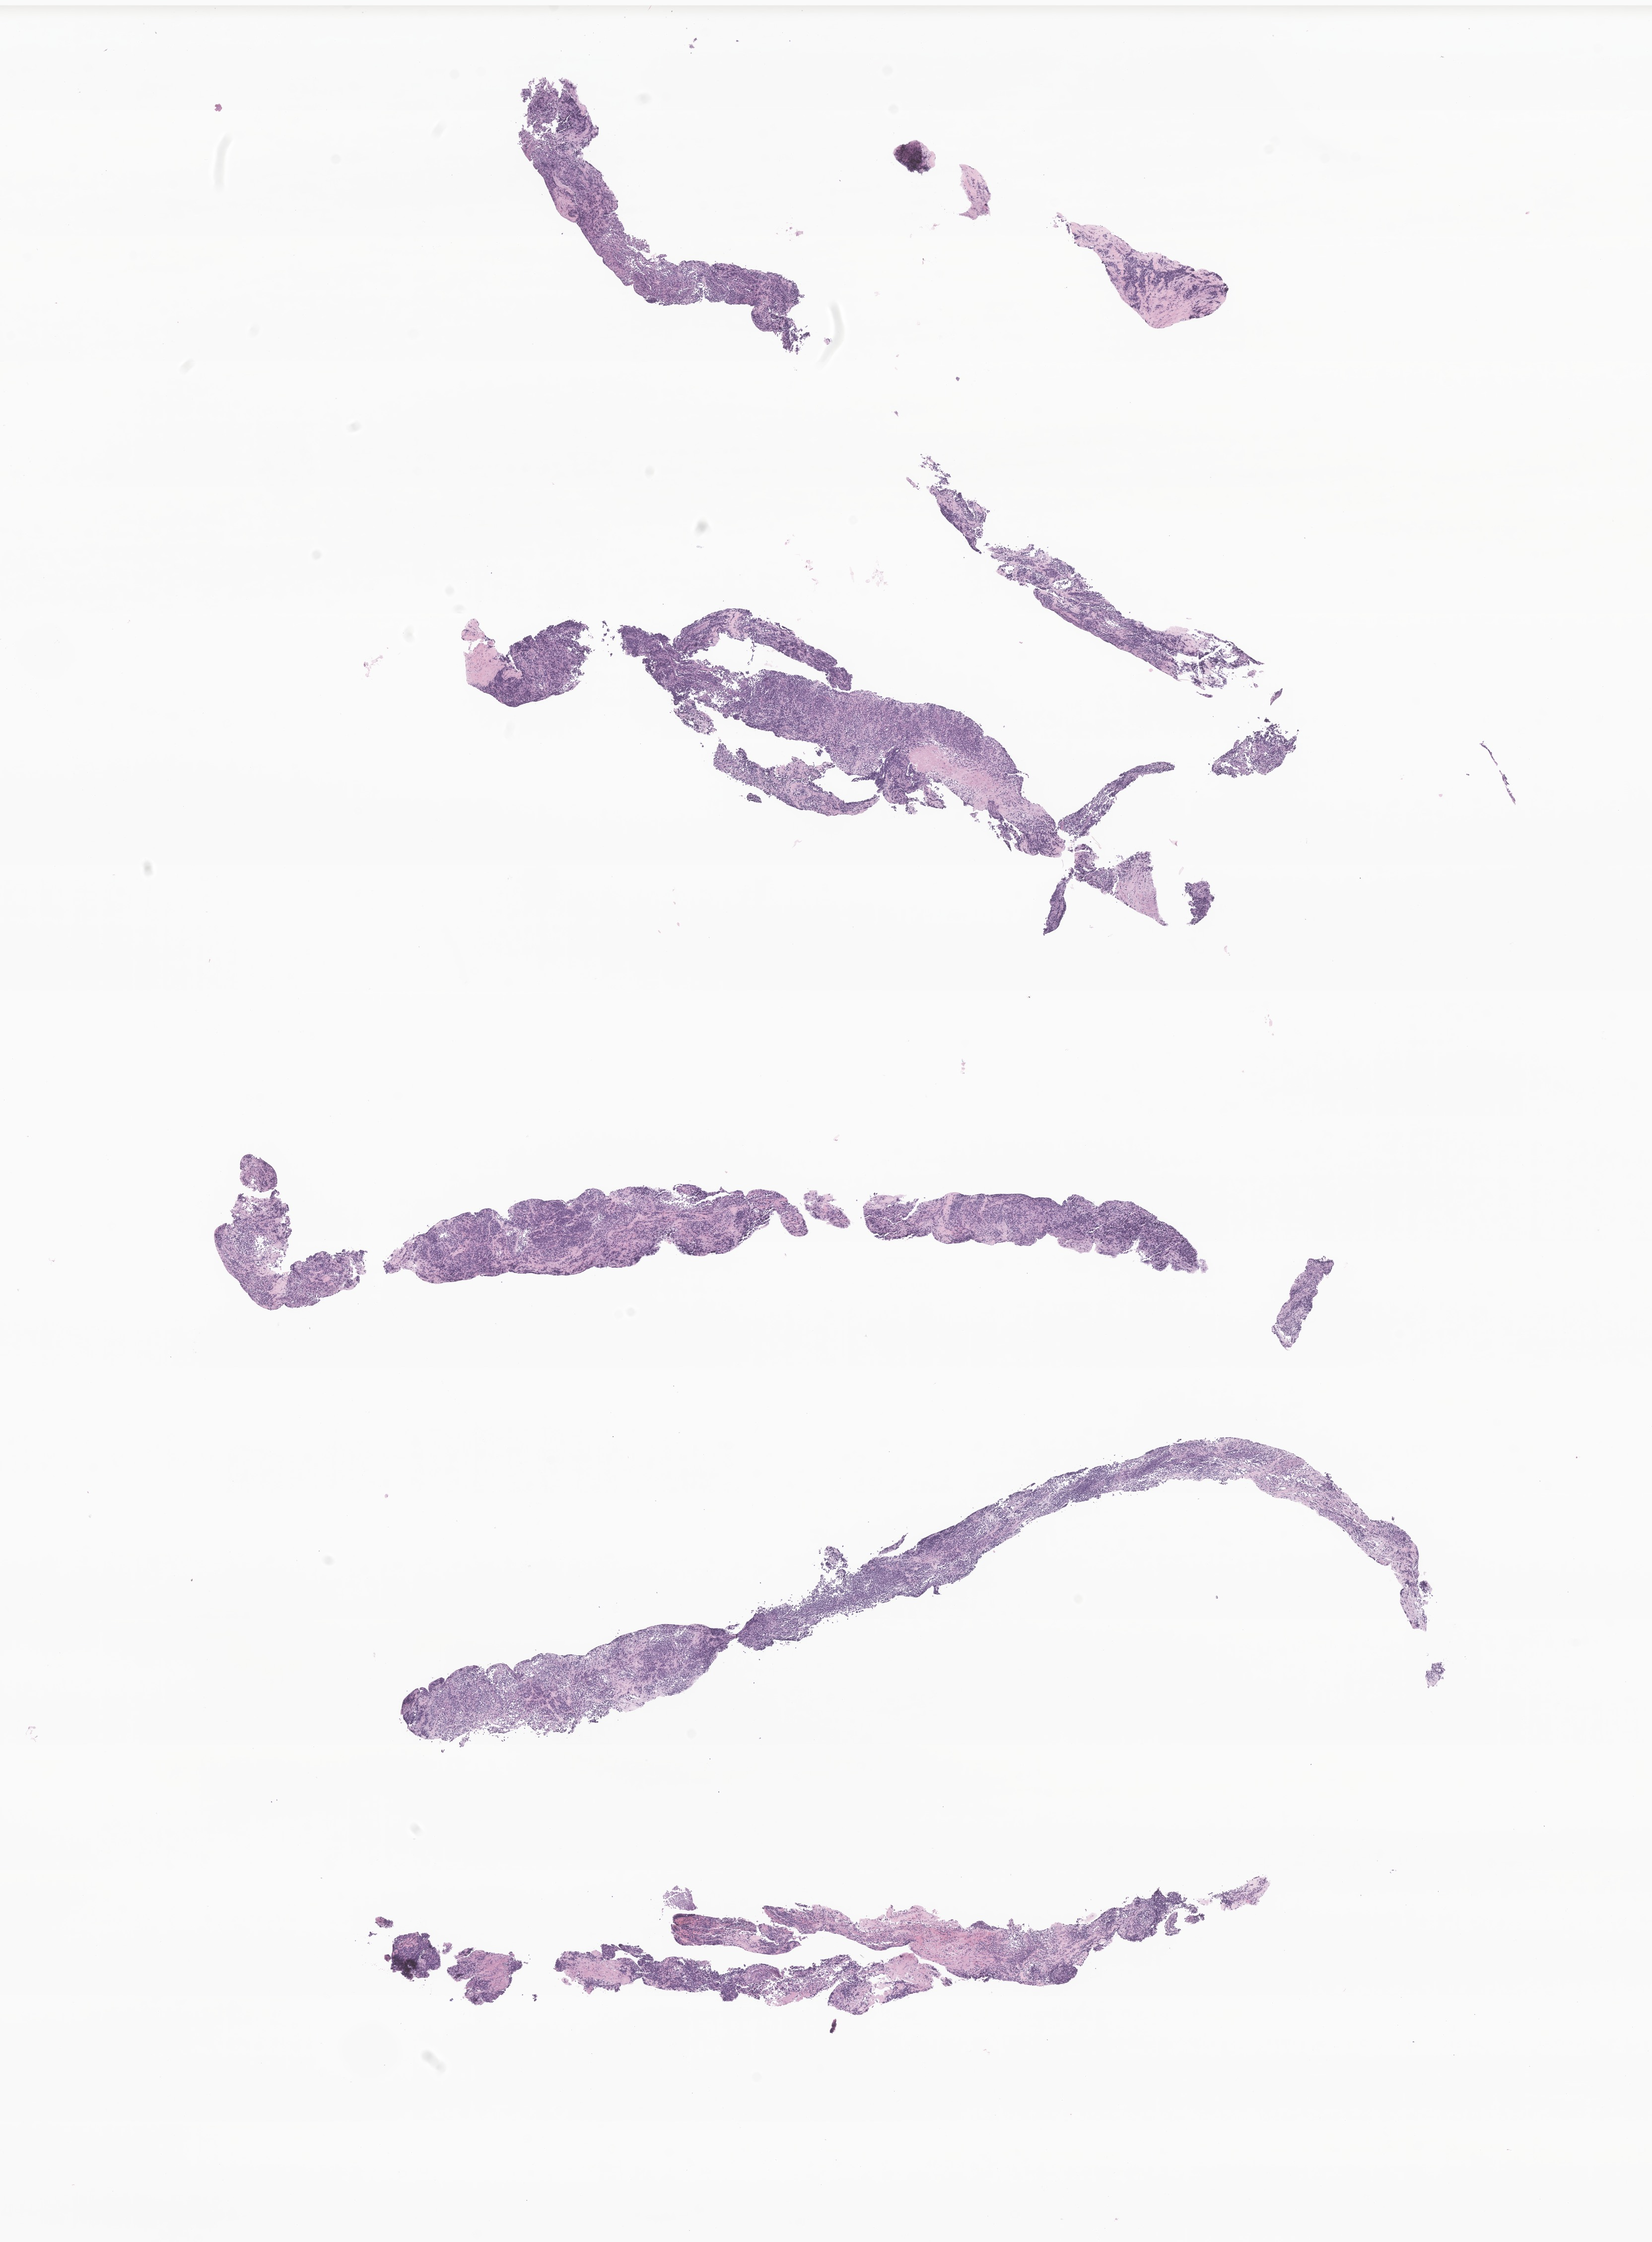
Whole-slide image, hematoxylin and eosin (H&E) stain of tumor tissue from the soft tissue of lower extremity, a low-resolution overview of the entire scanned area, about 14.0 x 19.0 mm, formalin-fixed, paraffin-embedded (FFPE) tissue. Female patient, age 95 months (7 years 11 months).
Diagnosis: Alveolar rhabdomyosarcoma.